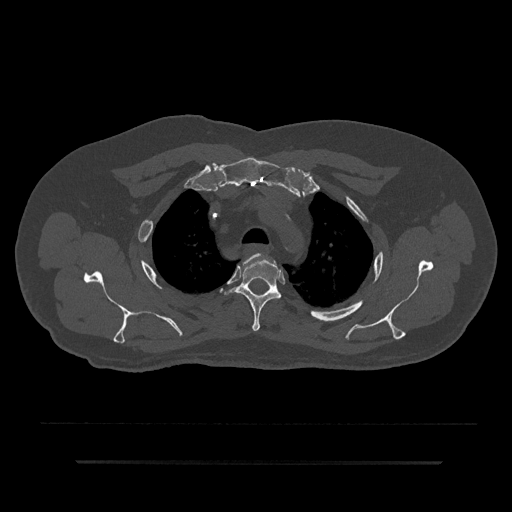
CT including the spine, one axial slice; position 658 of 797 along the scan axis; reconstruction kernel Br40s/3; bone window (W 1800 / L 400 HU); 0.5 mm slice thickness; 512 × 512 image matrix, field of view 464 × 464 mm. Patient: male, 59 years. From the clinical record (not read from this slice): primary cancer: bile ducts.
Outlined on this slice (semi-automatically segmented with operator editing):
- T2 vertebra: bounding box [x1, y1, x2, y2] px = [238, 258, 271, 266]
- T3 vertebra: [226, 254, 281, 332]